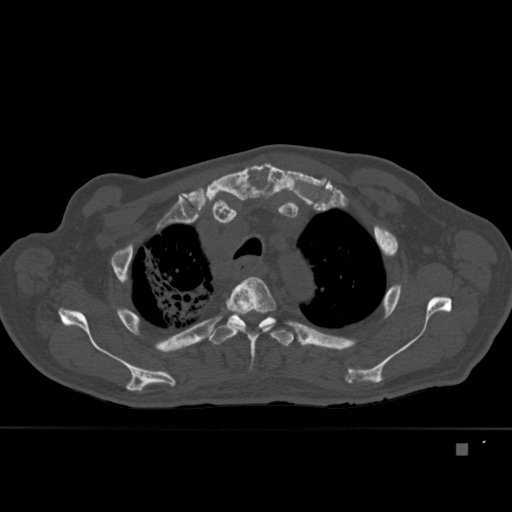
CT including the spine, one axial slice. Position 329 of 451 along the scan axis. Bone window (W 1800 / L 400 HU). 512 × 512 image matrix, field of view 378 × 378 mm. Patient: male, 75 years. Case-level facts recorded for this patient, not image findings: primary cancer: prostate.
Outlined on this slice (semi-automatically segmented with operator editing):
- T3 vertebra: bounding box (x1, y1, x2, y2) in pixels: (226, 277, 277, 369)
- T4 vertebra: (208, 310, 294, 347)